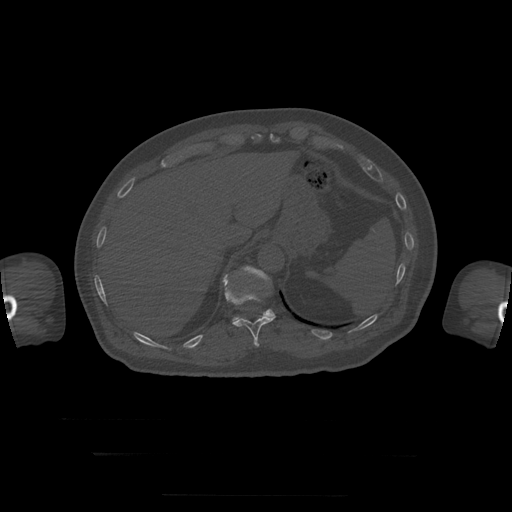
CT including the spine, one axial slice; position 92 of 397 along the scan axis; reconstruction kernel STANDARD; bone window (W 1800 / L 400 HU); 1.25 mm slice thickness; 512 × 512 image matrix, field of view 510 × 510 mm. Patient age 73 years. Case-level facts recorded for this patient, not image findings: primary cancer: prostate.
Annotated regions visible in this slice (semi-automatically segmented with operator editing):
- T11 vertebra: box from (x=223, y=274) to (x=276, y=347) px
- T12 vertebra: (x=233, y=266)–(x=275, y=322)